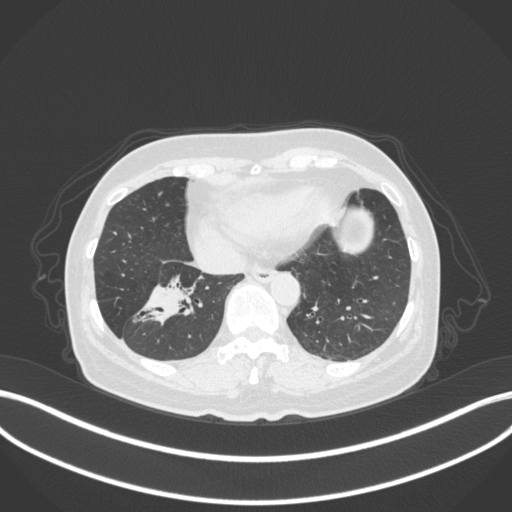
Chest CT, one axial slice; slice 115 of 429 in the series (ordered by position); reconstruction kernel B31f; 120 kVp; lung window (W 1500 / L -600 HU); 1 mm slice thickness; 512 × 512 image matrix, field of view 400 × 400 mm. Female patient, age 67 years. From the clinical record (not read from this slice): clinical TNM (as recorded): T1c N1 M0.
Structures marked on this image (bounding box drawn by a radiologist):
- lung tumour (recorded histology: adenocarcinoma): bounding box <126,268,210,335> (left, top, right, bottom; pixels)